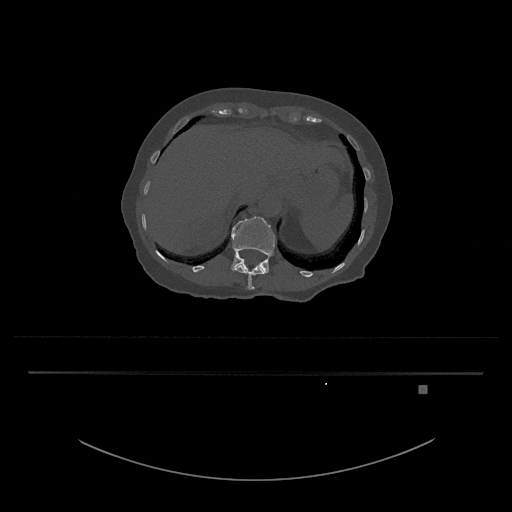
CT including the spine, one axial slice; position 581 of 797 along the scan axis; 120 kVp; bone window (W 1800 / L 400 HU); 0.5 mm slice thickness; 512 × 512 image matrix, field of view 500 × 500 mm. Patient: female, 57 years. Case-level facts recorded for this patient, not image findings: primary cancer: cervical.
Annotated regions visible in this slice (semi-automatically segmented with operator editing):
- L1 vertebra: bounding box [x1, y1, x2, y2] px = [231, 216, 275, 274]
- T12 vertebra: [235, 262, 265, 290]